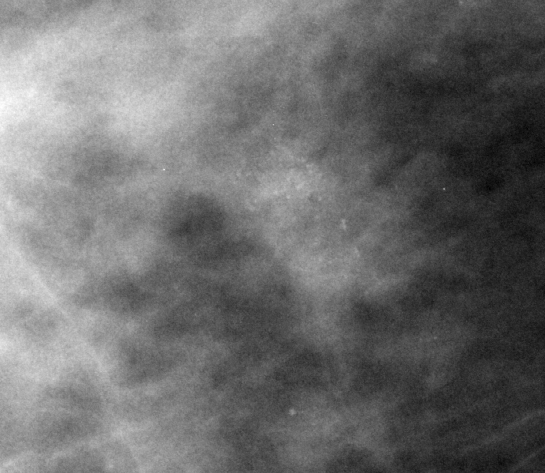
Cropped region of a digitized screen-film mammogram centred on a radiologist-marked abnormality; right breast; CC view; BI-RADS breast density category 3 (scale 1–4).
Calcifications, morphology amorphous, distribution clustered; BI-RADS assessment category 4; subtlety rating 2 on a 1 (subtle) to 5 (obvious) scale; pathology (as recorded): benign.